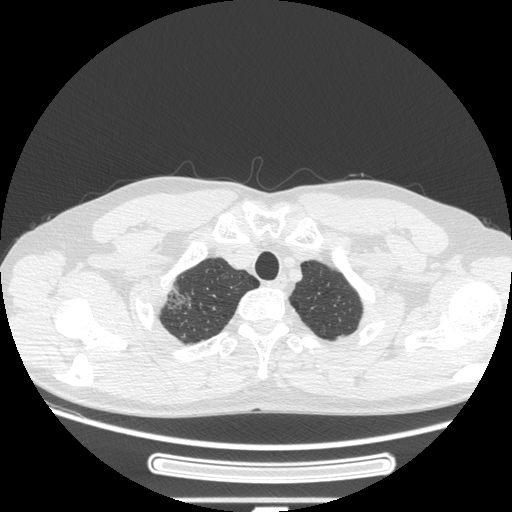
Chest CT, one axial slice. Slice 237 of 269 in the series (ordered by position). Reconstruction kernel STANDARD. Lung window (W 1500 / L -600 HU). 1.25 mm slice thickness. 512 × 512 image matrix, field of view 382 × 382 mm. Male patient, age 53 years. From the clinical record (not read from this slice): clinical TNM (as recorded): T1c N0 M0; histopathological grade: G2.
Outlined on this slice (bounding box drawn by a radiologist):
- lung tumour (recorded histology: adenocarcinoma): bounding box (x1, y1, x2, y2) in pixels: (161, 278, 194, 320)